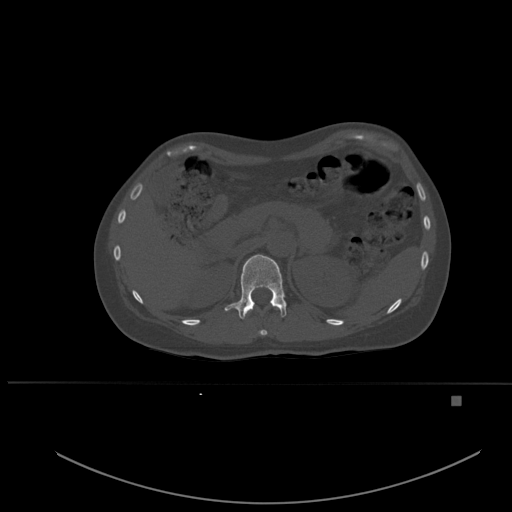
CT including the spine, one axial slice; position 258 of 651 along the scan axis; bone window (W 1800 / L 400 HU); 512 × 512 image matrix, field of view 443 × 443 mm. Patient: female, 49 years. From the clinical record (not read from this slice): primary cancer: breast; vertebrae with lytic lesions (as recorded): L3, T12, L4.
Annotated regions visible in this slice (semi-automatic segmentation, software-assisted and operator-edited):
- T11 vertebra: bounding box [x1, y1, x2, y2] px = [259, 330, 268, 335]
- T12 vertebra: [225, 254, 287, 319]